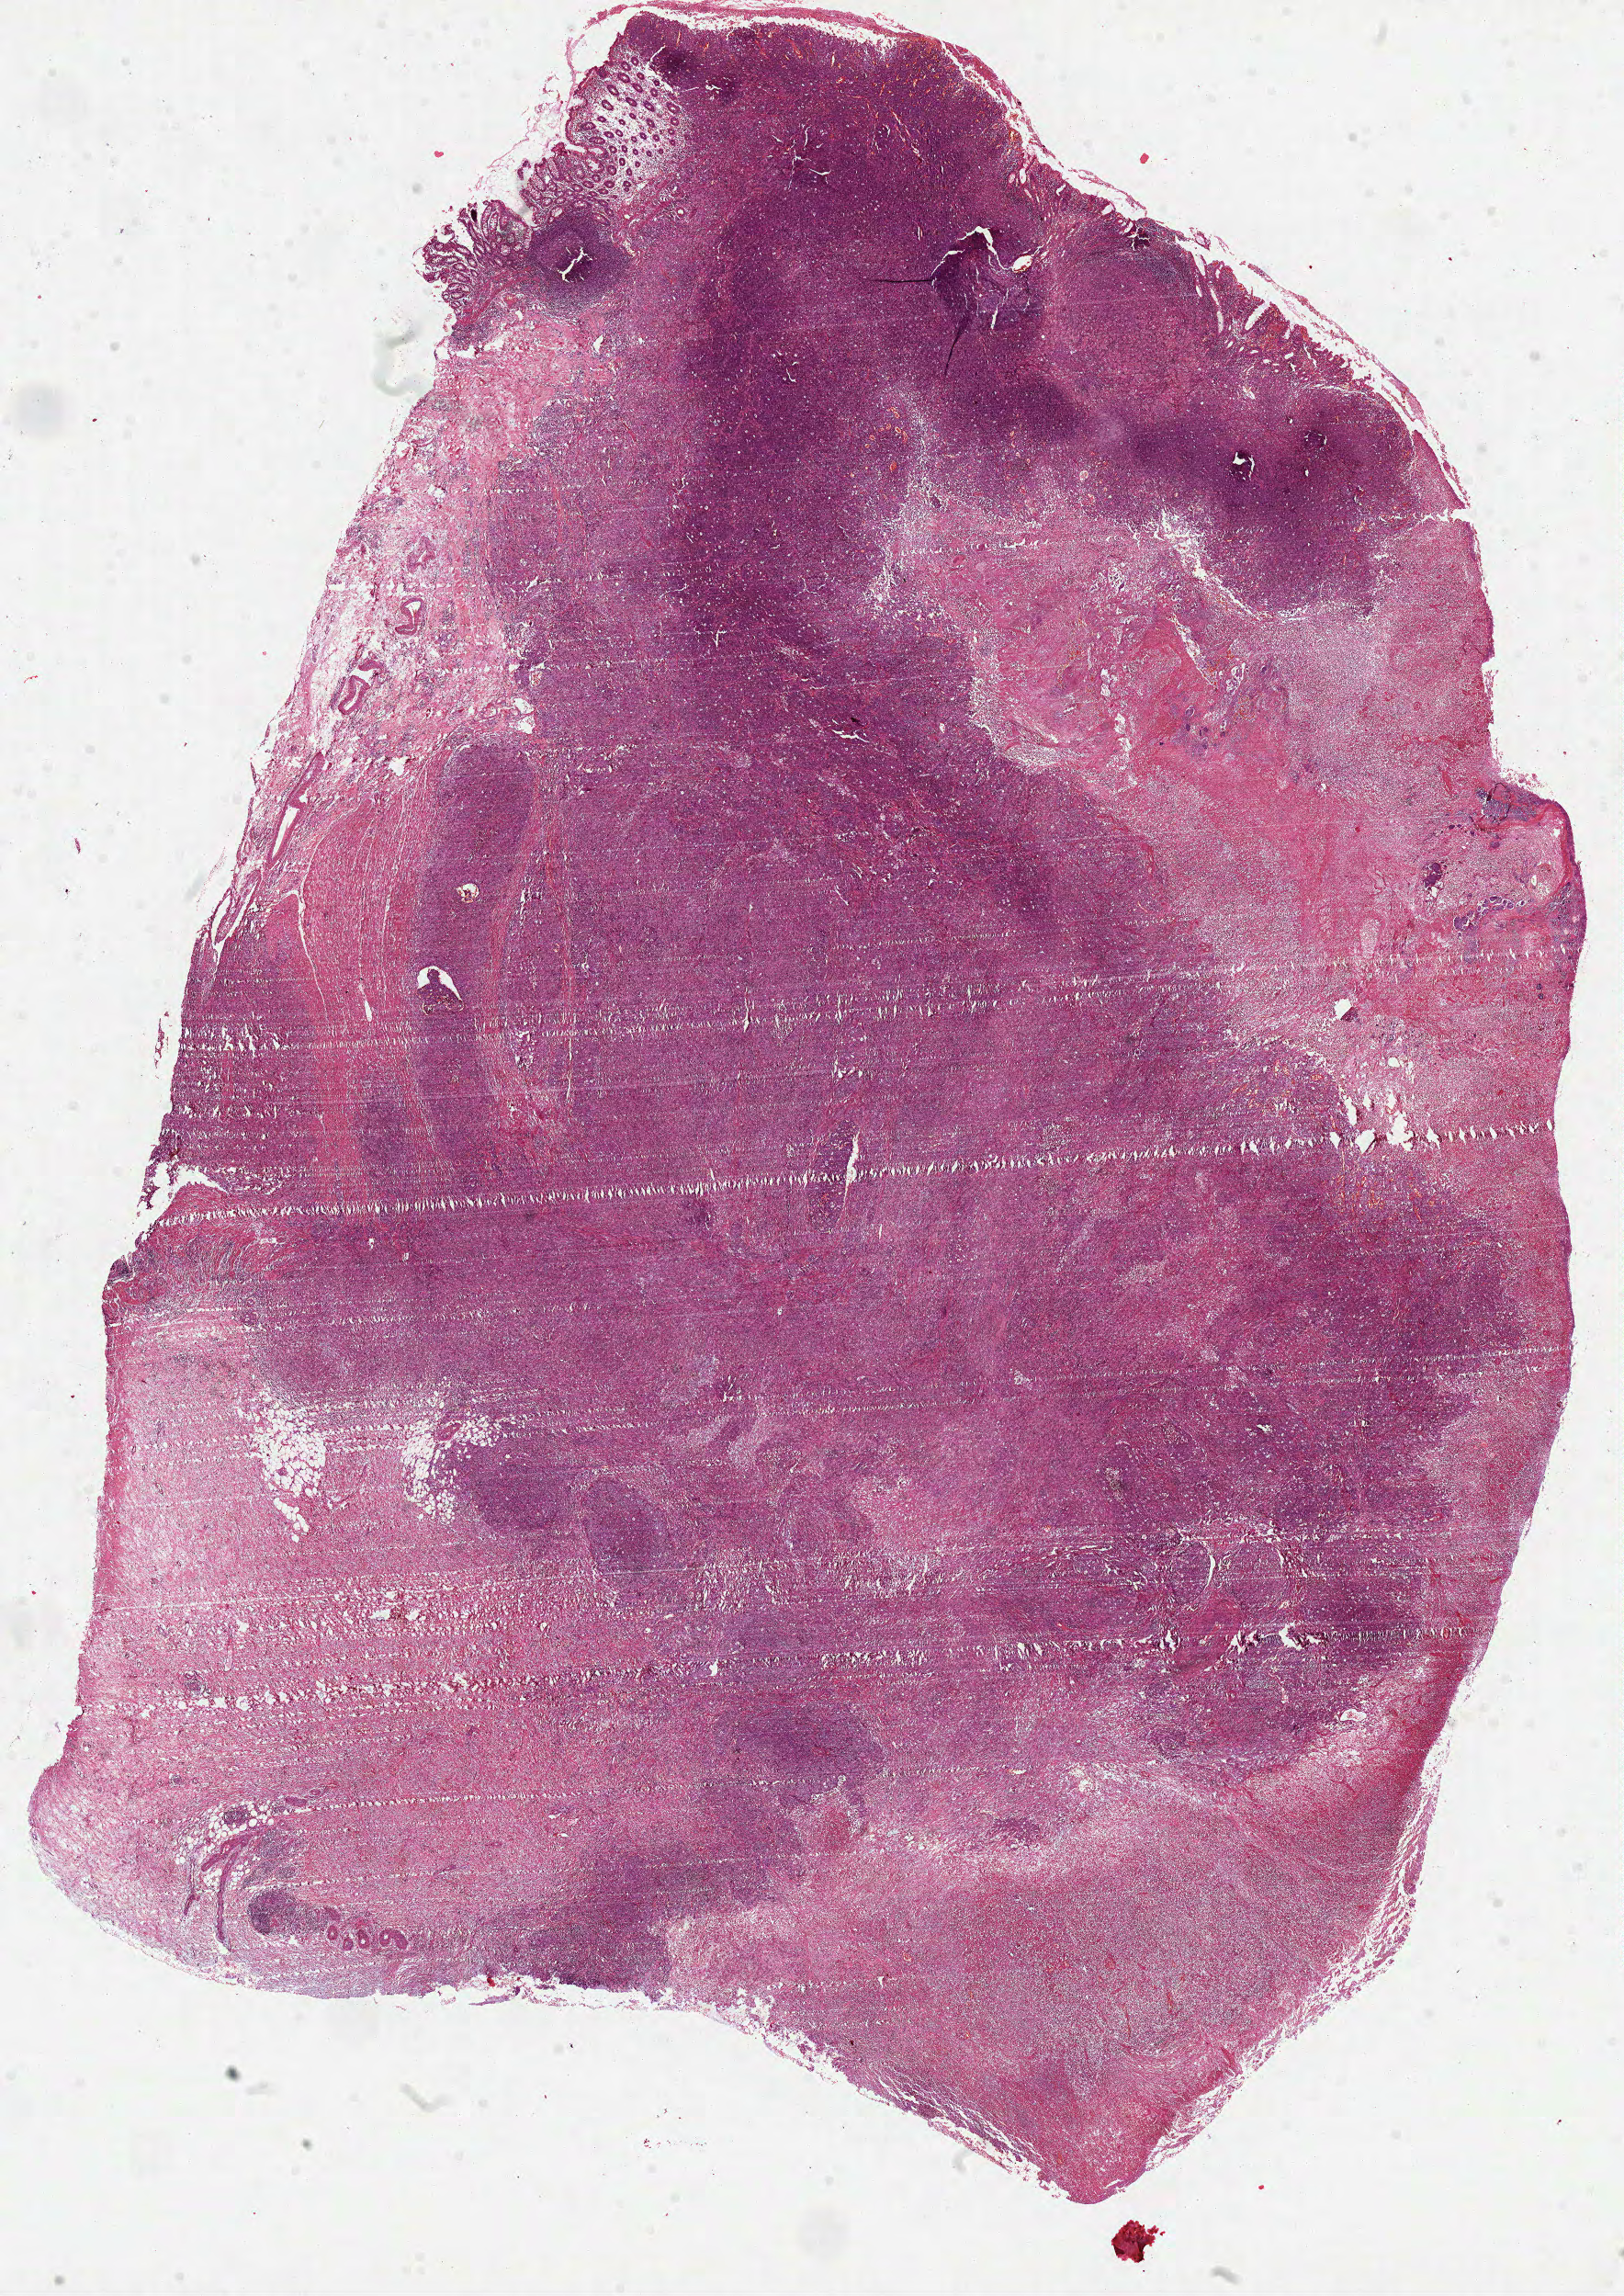
Digitized H&E-stained tissue section (whole slide), a low-resolution overview of the entire scanned area, about 14.3 x 20.2 mm (from a 40x scan); FFPE section; sample: primary tumour, colon. Male, age 46 years at initial diagnosis.
TNM: T3 N0 M0. Pathologic diagnosis: Adenocarcinoma, NOS. AJCC pathologic stage: IIA (6th edition).